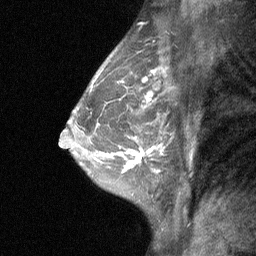
Breast MRI (dynamic contrast-enhanced), one sagittal slice. Slice 42 of 64 in the series (ordered by position). Dynamic contrast-enhanced study with each time point stored as its own series, time point 2 of 3 at this slice position (early post-contrast, ordered by acquisition time). 1.5 T. TE 4.8 ms, TR 27 ms. 2 mm slice thickness. 256 × 256 image matrix, field of view 180 × 180 mm. Patient: female, 47 years. Case-level facts recorded for this patient, not image findings: setting: breast cancer imaged before/during neoadjuvant chemotherapy; receptor status: HR-positive, HER2-negative.
Annotated regions visible in this slice (semi-automatically segmented with operator editing):
- analysis volume of interest (the breast-tissue region the enhancement analysis was run in; not a lesion): bounding box <104,138,163,198> (left, top, right, bottom; pixels)
- tumour enhancement mask (voxels above the 90 % enhancement threshold inside the analysis volume of interest): <108,147,154,172>